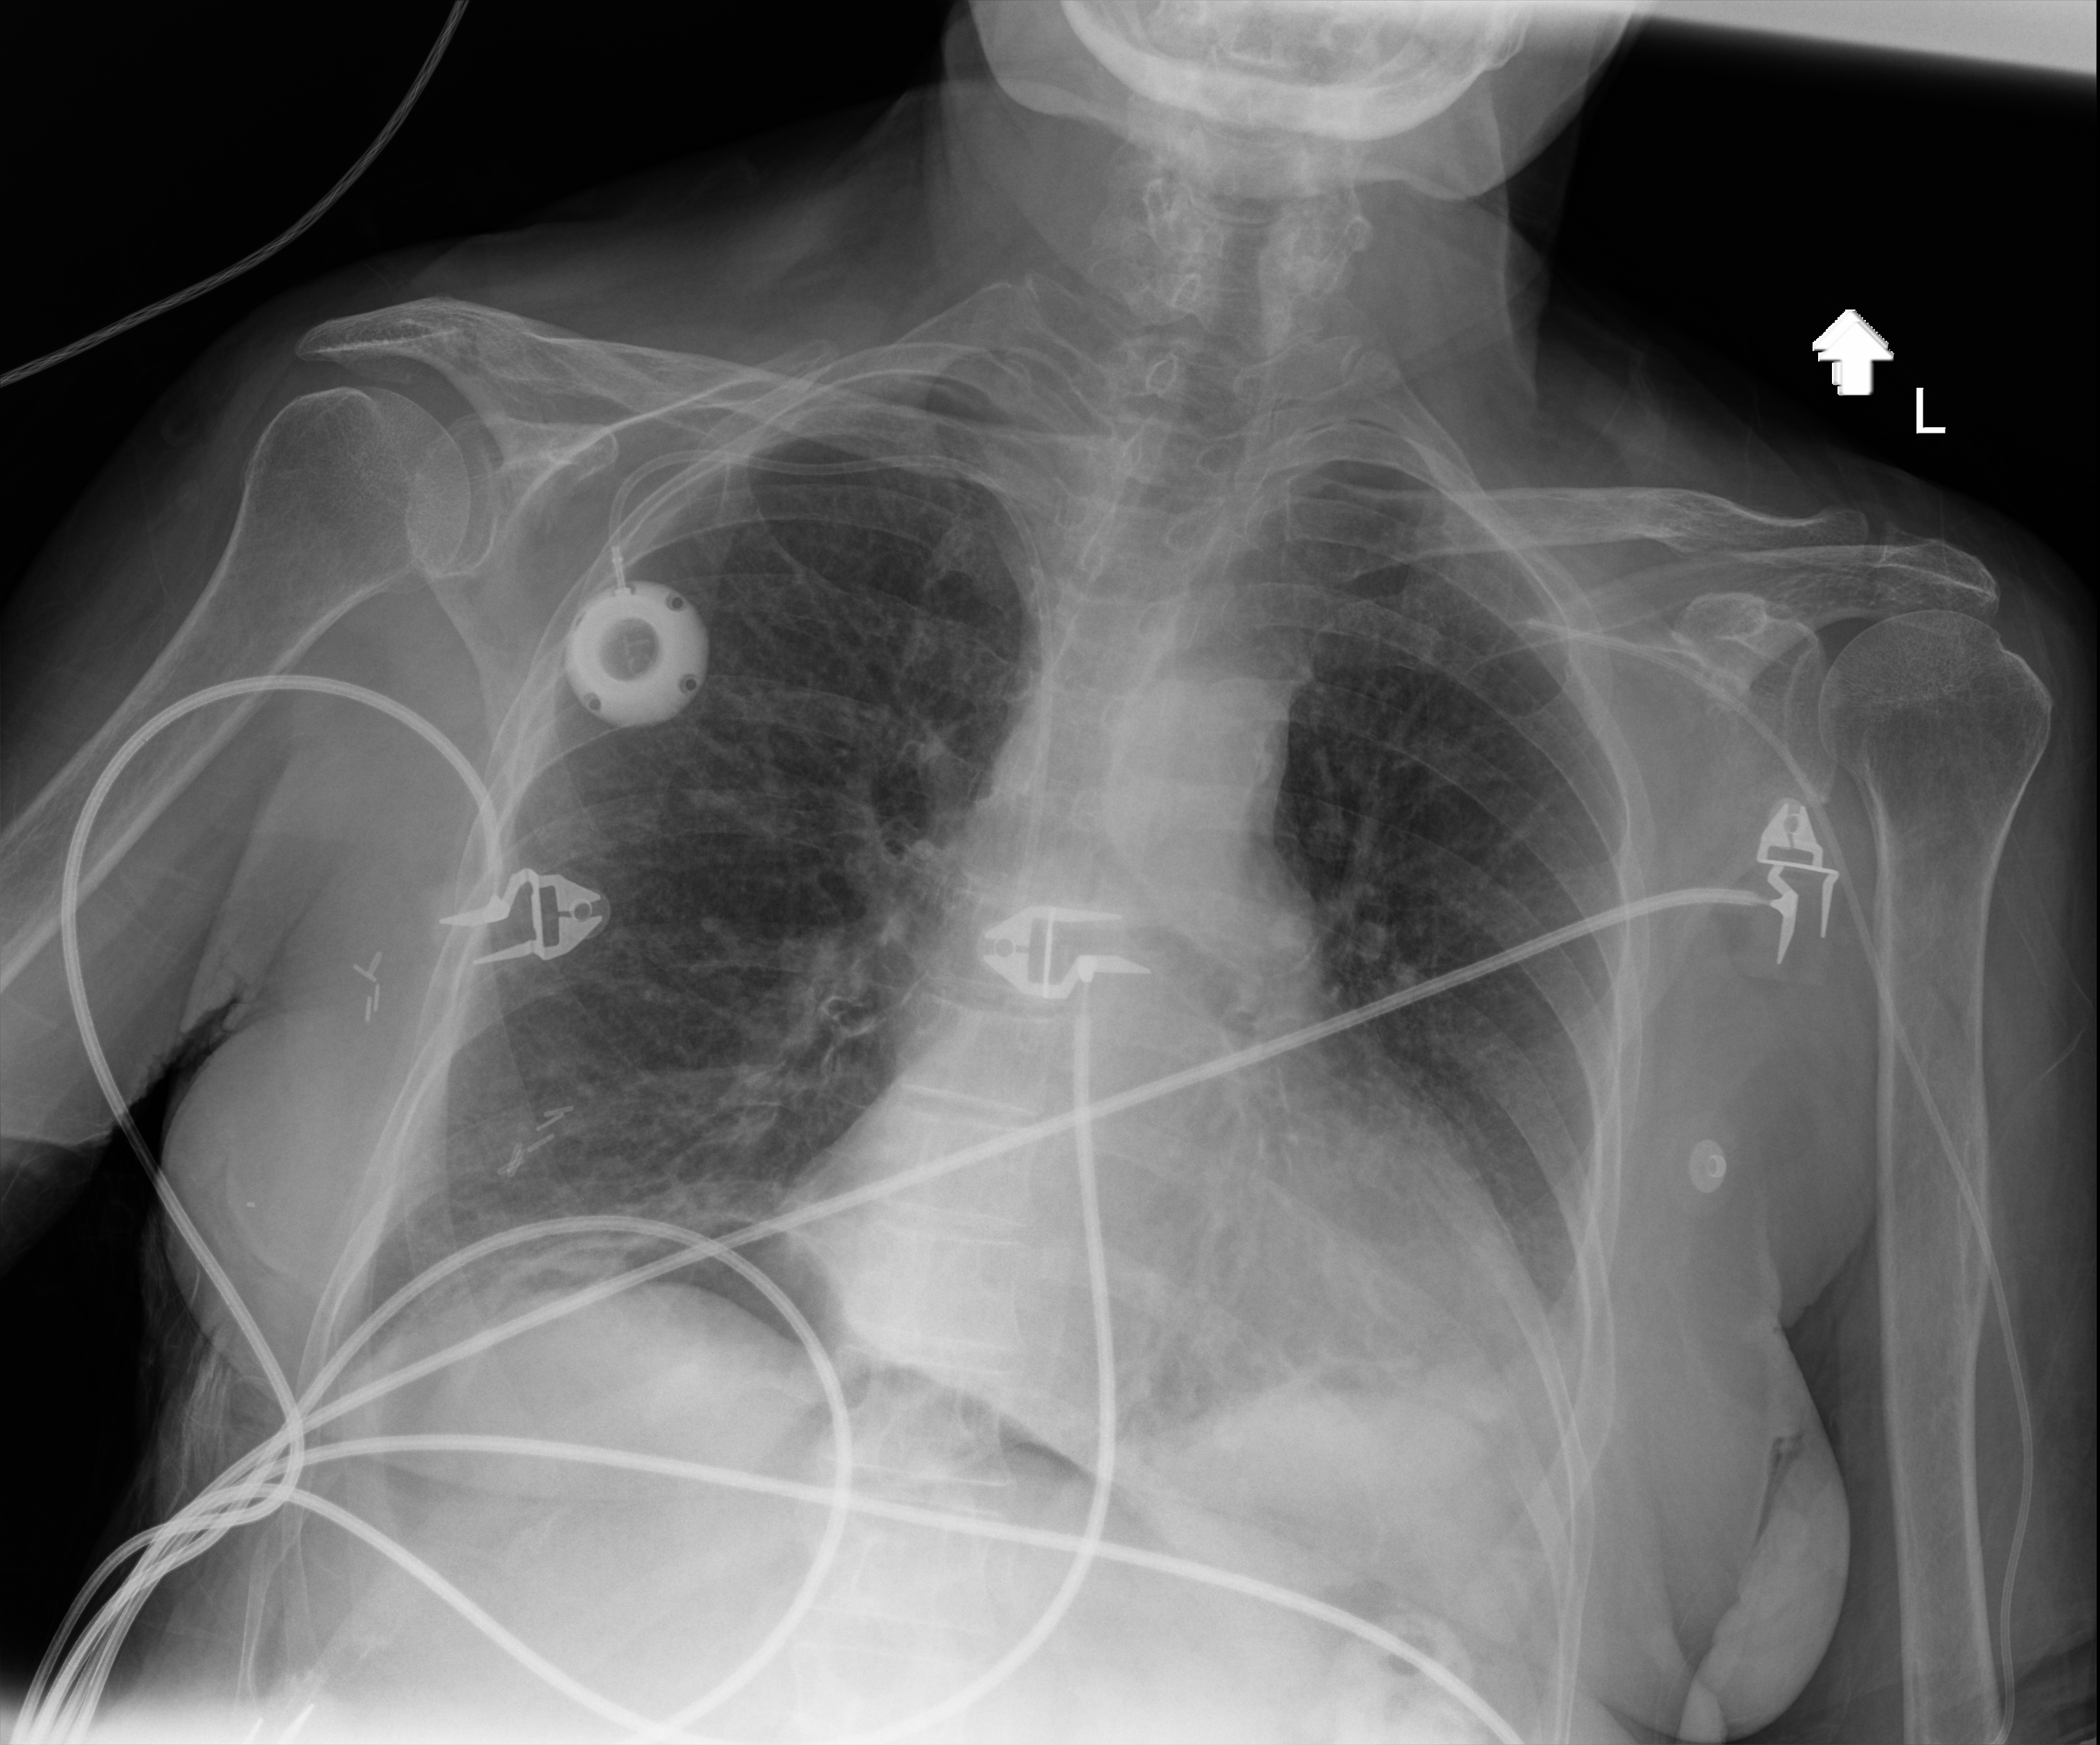
Chest X-ray (portable); anteroposterior (AP) projection. Patient hospitalised with COVID-19; female, aged 60–74 years.
Admission-level facts for this patient (not findings on this image; timing relative to this image not recorded): length of hospital stay: 43 days.